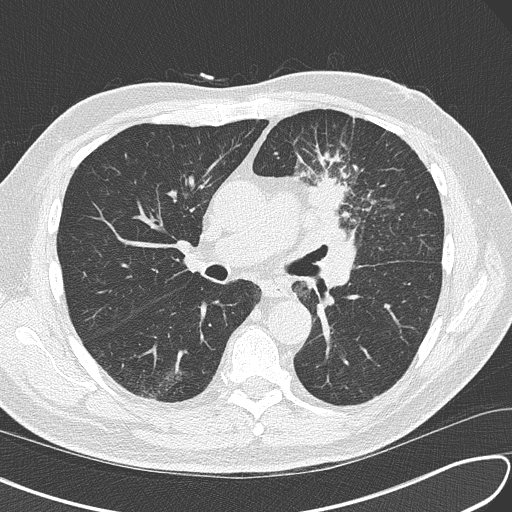
Axial slice from a low-dose chest CT screening exam; third annual screen; lung window (W 1500 / L -600 HU); 2 mm slice thickness; slice 68 of 156 in the series; 512 × 512 image matrix, field of view 340 × 340 mm. Male, age 67 years at enrolment. Current smoker at enrolment.
• Expert-annotated lung lesion, bounding box (x1, y1, x2, y2) in pixels: (293, 157, 393, 246).
• Reader record for this screening exam (exam-level; its link to the box is not recorded): non-calcified nodule or mass ≥4 mm, left upper lobe, 30 × 23 mm, soft tissue attenuation, pre-existing on the prior screen: no.
• Official screen result: positive, other.
• Participant outcome: lung cancer diagnosed 41 days after this screen — small cell carcinoma, NOS, left upper lobe, stage IV (AJCC 6th edition), 30 mm at pathology.